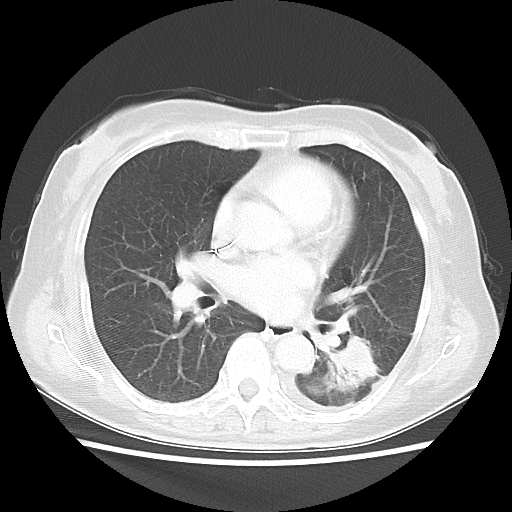
Chest CT, one axial slice; slice 18 of 40 in the series (ordered by position); reconstruction kernel LUNG; lung window (W 1500 / L -600 HU); 5 mm slice thickness; 512 × 512 image matrix. Patient: female, 69 years. From the clinical record (not read from this slice): clinical TNM (as recorded): T1c N0 M0.
Outlined on this slice (bounding box drawn by a radiologist):
- lung tumour (recorded histology: adenocarcinoma): box from (x=323, y=331) to (x=387, y=400) px